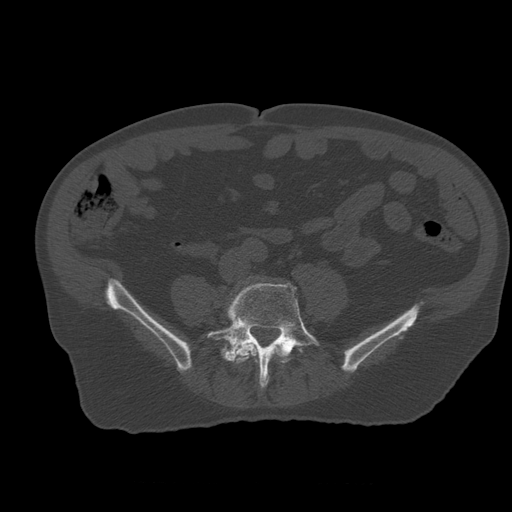
CT including the spine, one axial slice. Slice 147 of 399 in the series (ordered by position). Reconstruction kernel STANDARD. 120 kVp. Bone window (W 1800 / L 400 HU). 1.25 mm slice thickness. 512 × 512 image matrix, field of view 407 × 407 mm. Patient age 73 years. Case-level facts recorded for this patient, not image findings: primary cancer: prostate; vertebrae with lytic lesions (as recorded): L2.
Outlined on this slice (semi-automatic segmentation, software-assisted and operator-edited):
- L4 vertebra: box from (x=232, y=343) to (x=284, y=364) px
- L5 vertebra: (x=207, y=283)–(x=320, y=388)